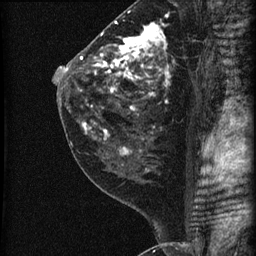
Breast MRI (dynamic contrast-enhanced), one sagittal slice. Slice 33 of 60 in the series (ordered by position). Dynamic contrast-enhanced series, image 2 of 3 at this slice position (ordered by acquisition). 1.5 T. TE 4.2 ms, TR 22.7 ms. 1.8 mm slice thickness. 256 × 256 image matrix, field of view 180 × 180 mm. Female patient, age 45 years. Case-level facts recorded for this patient, not image findings: setting: breast cancer imaged before/during neoadjuvant chemotherapy; receptor status: HR-positive, HER2-negative.
Structures marked on this image (semi-automatic segmentation, software-assisted and operator-edited):
- analysis volume of interest (the breast-tissue region the enhancement analysis was run in; not a lesion): box from (x=74, y=11) to (x=205, y=140) px
- tumour enhancement mask (voxels above the 90 % enhancement threshold inside the analysis volume of interest): (x=80, y=22)–(x=168, y=132)